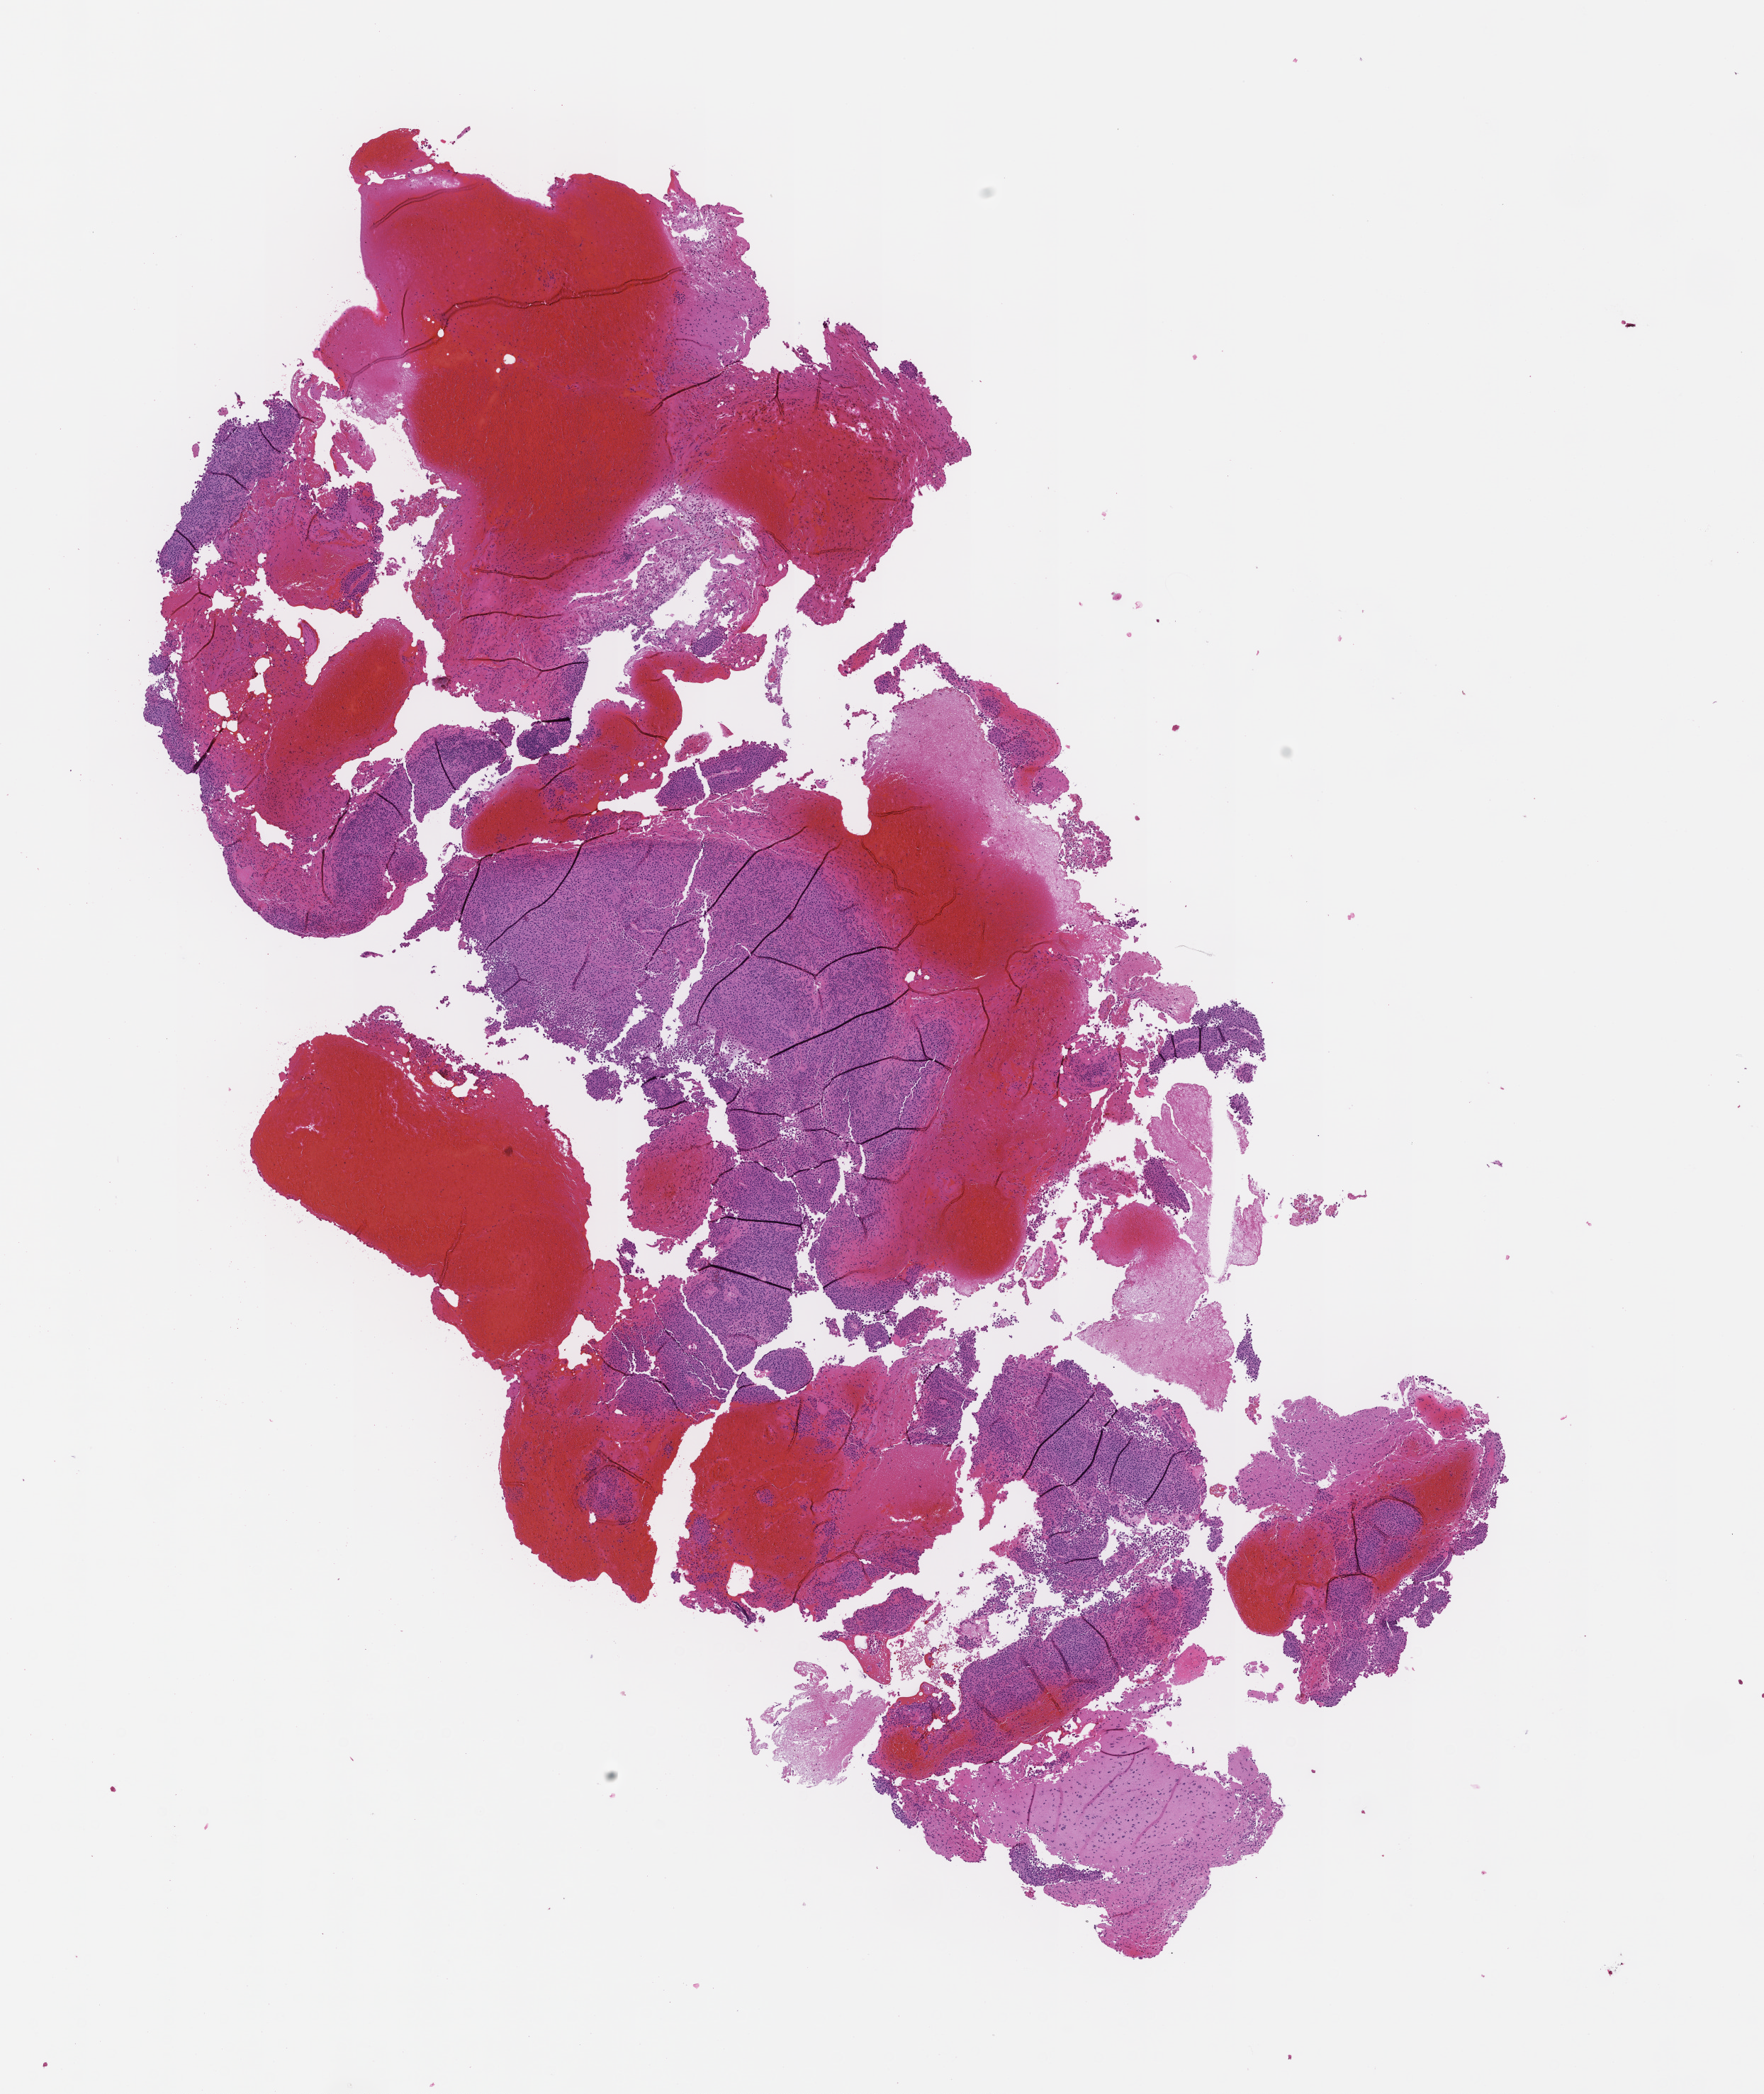
Whole-slide image, hematoxylin and eosin (H&E) stain — low-resolution overview of the scanned area, about 10.1 x 11.9 mm; formalin-fixed paraffin-embedded section. Male patient.
This section: metastatic tumor tissue. Primary diagnosis of the patient: Melanoma.